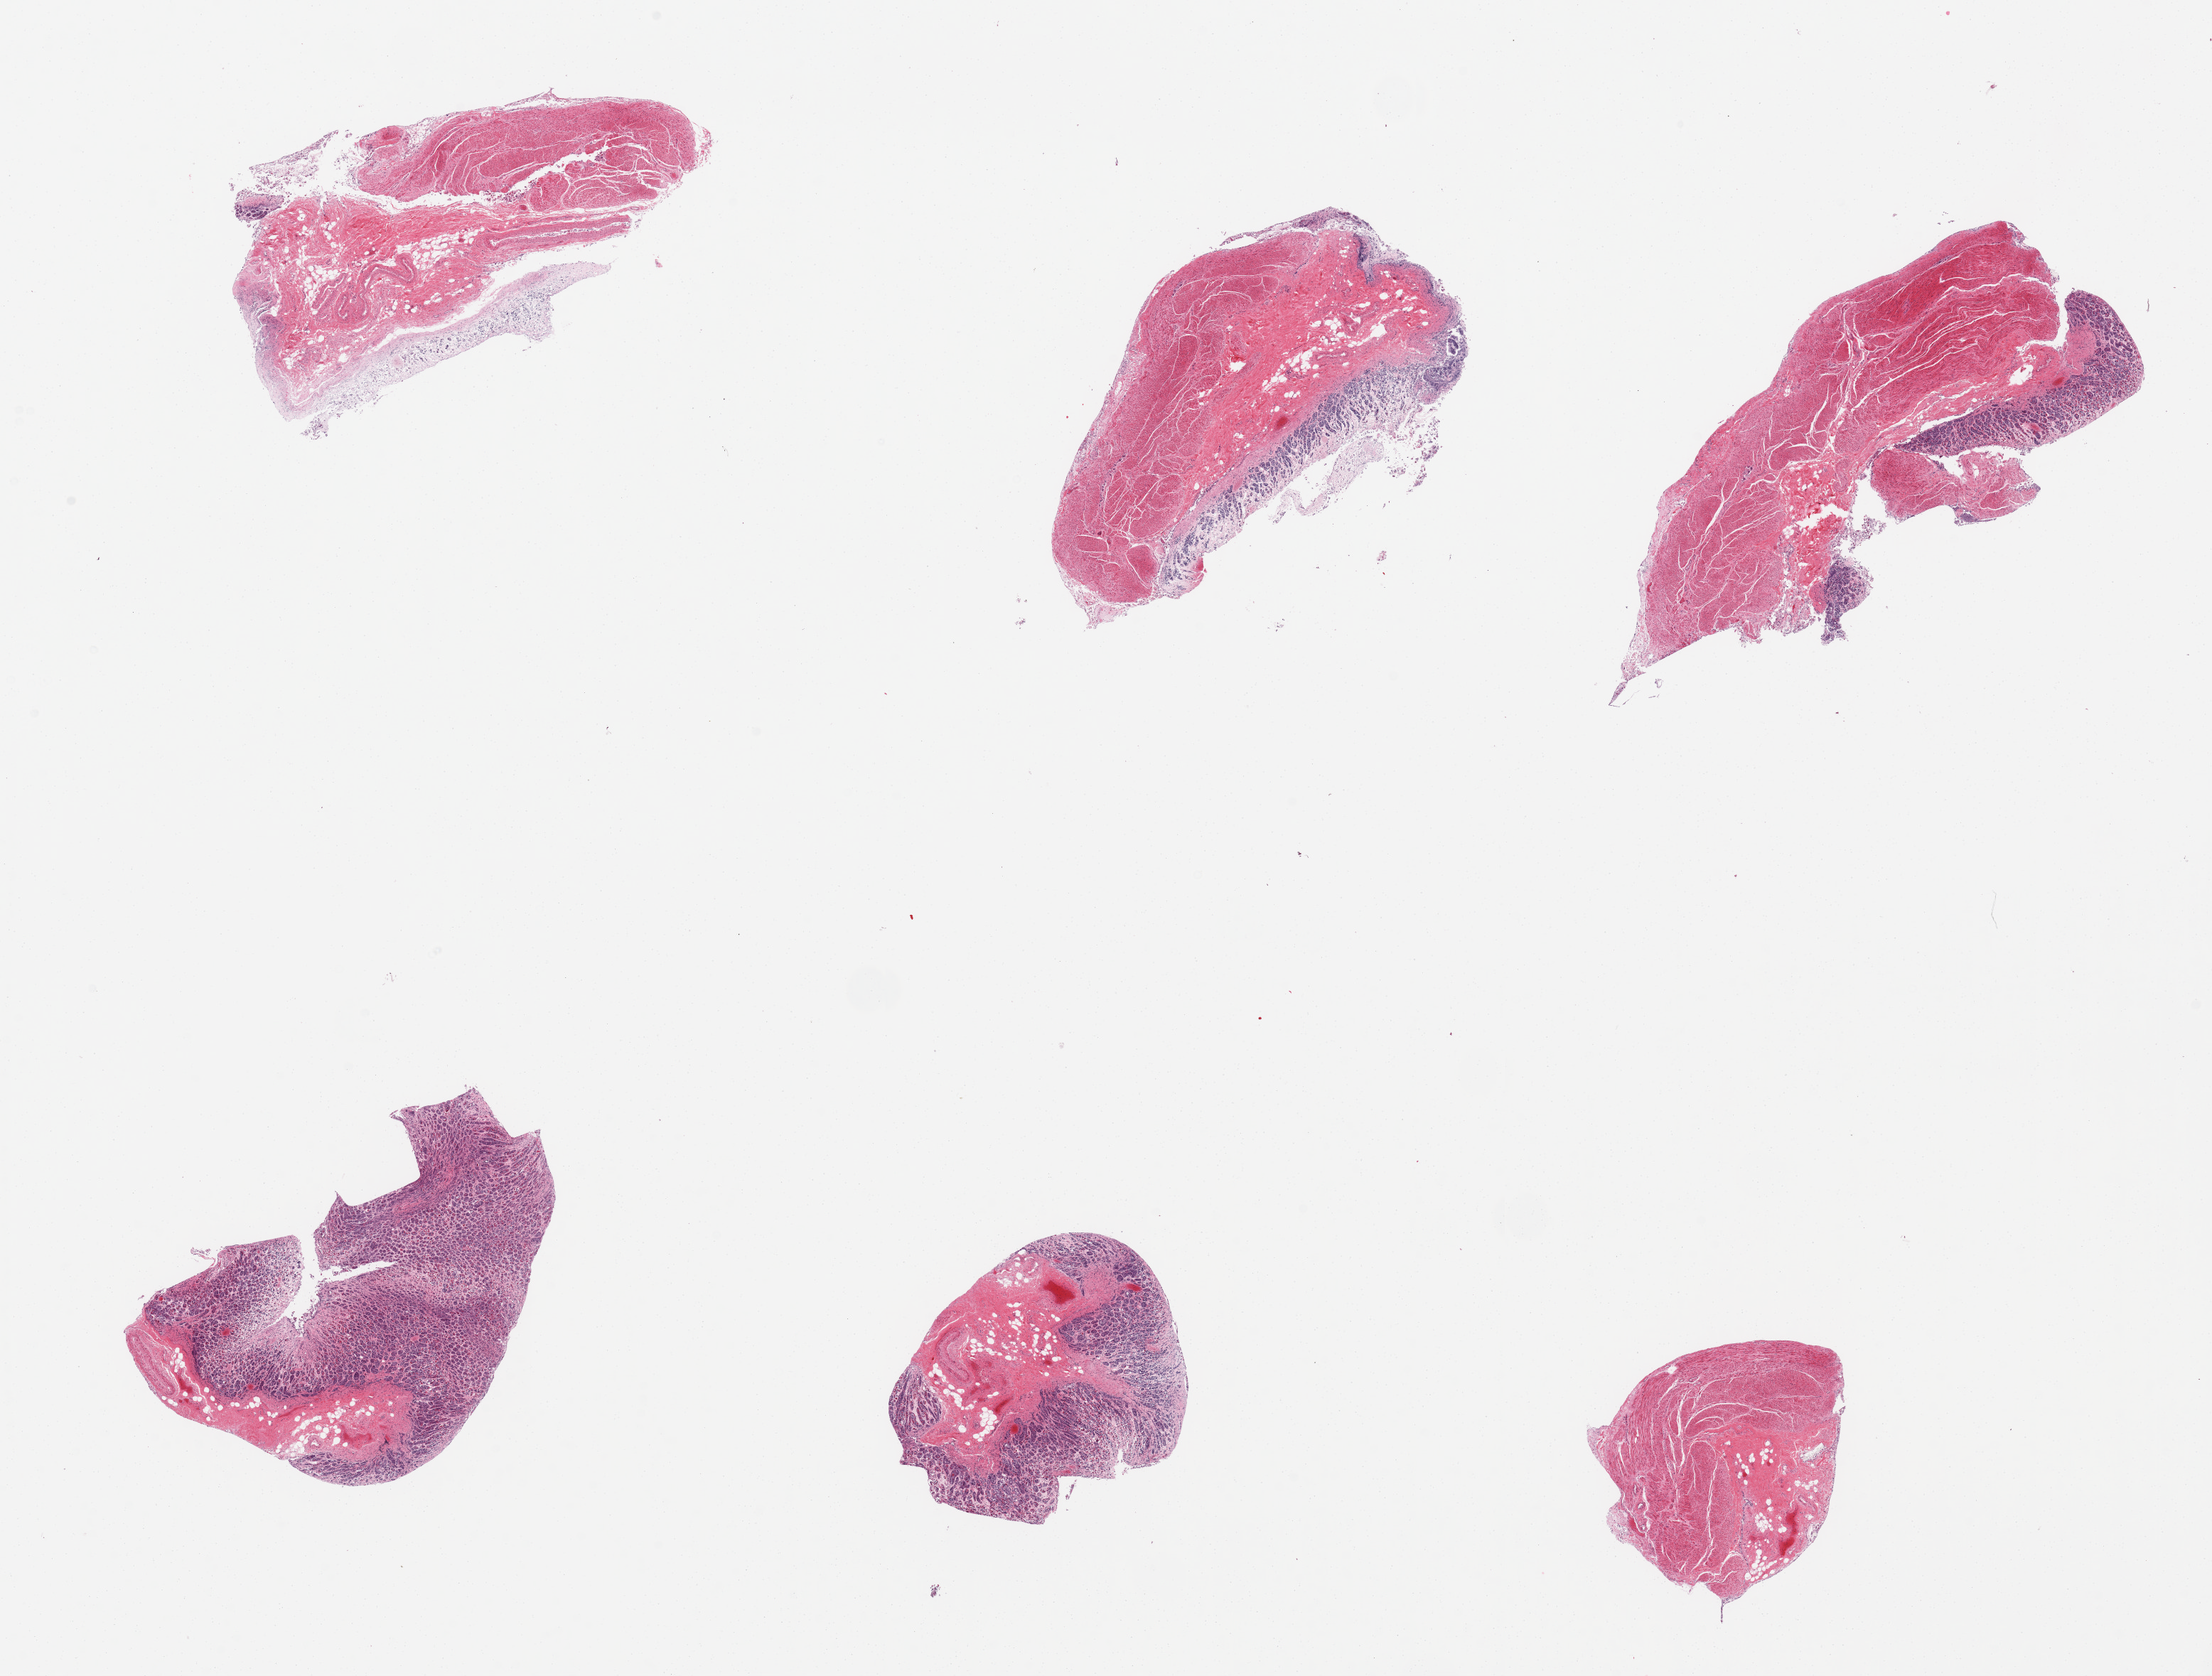
Digitized H&E-stained section, whole scanned area (about 24.6 x 18.6 mm) shown as a low-resolution overview. PAXgene-fixed paraffin-embedded (PFPE) section. Target tissue: stomach. Donor tissue sample. Male donor.
Review note (as recorded): 6 pieces with variable combination of mucosa/muscularis. Mucosa moderately to severely autolyzed, muscularis less so.